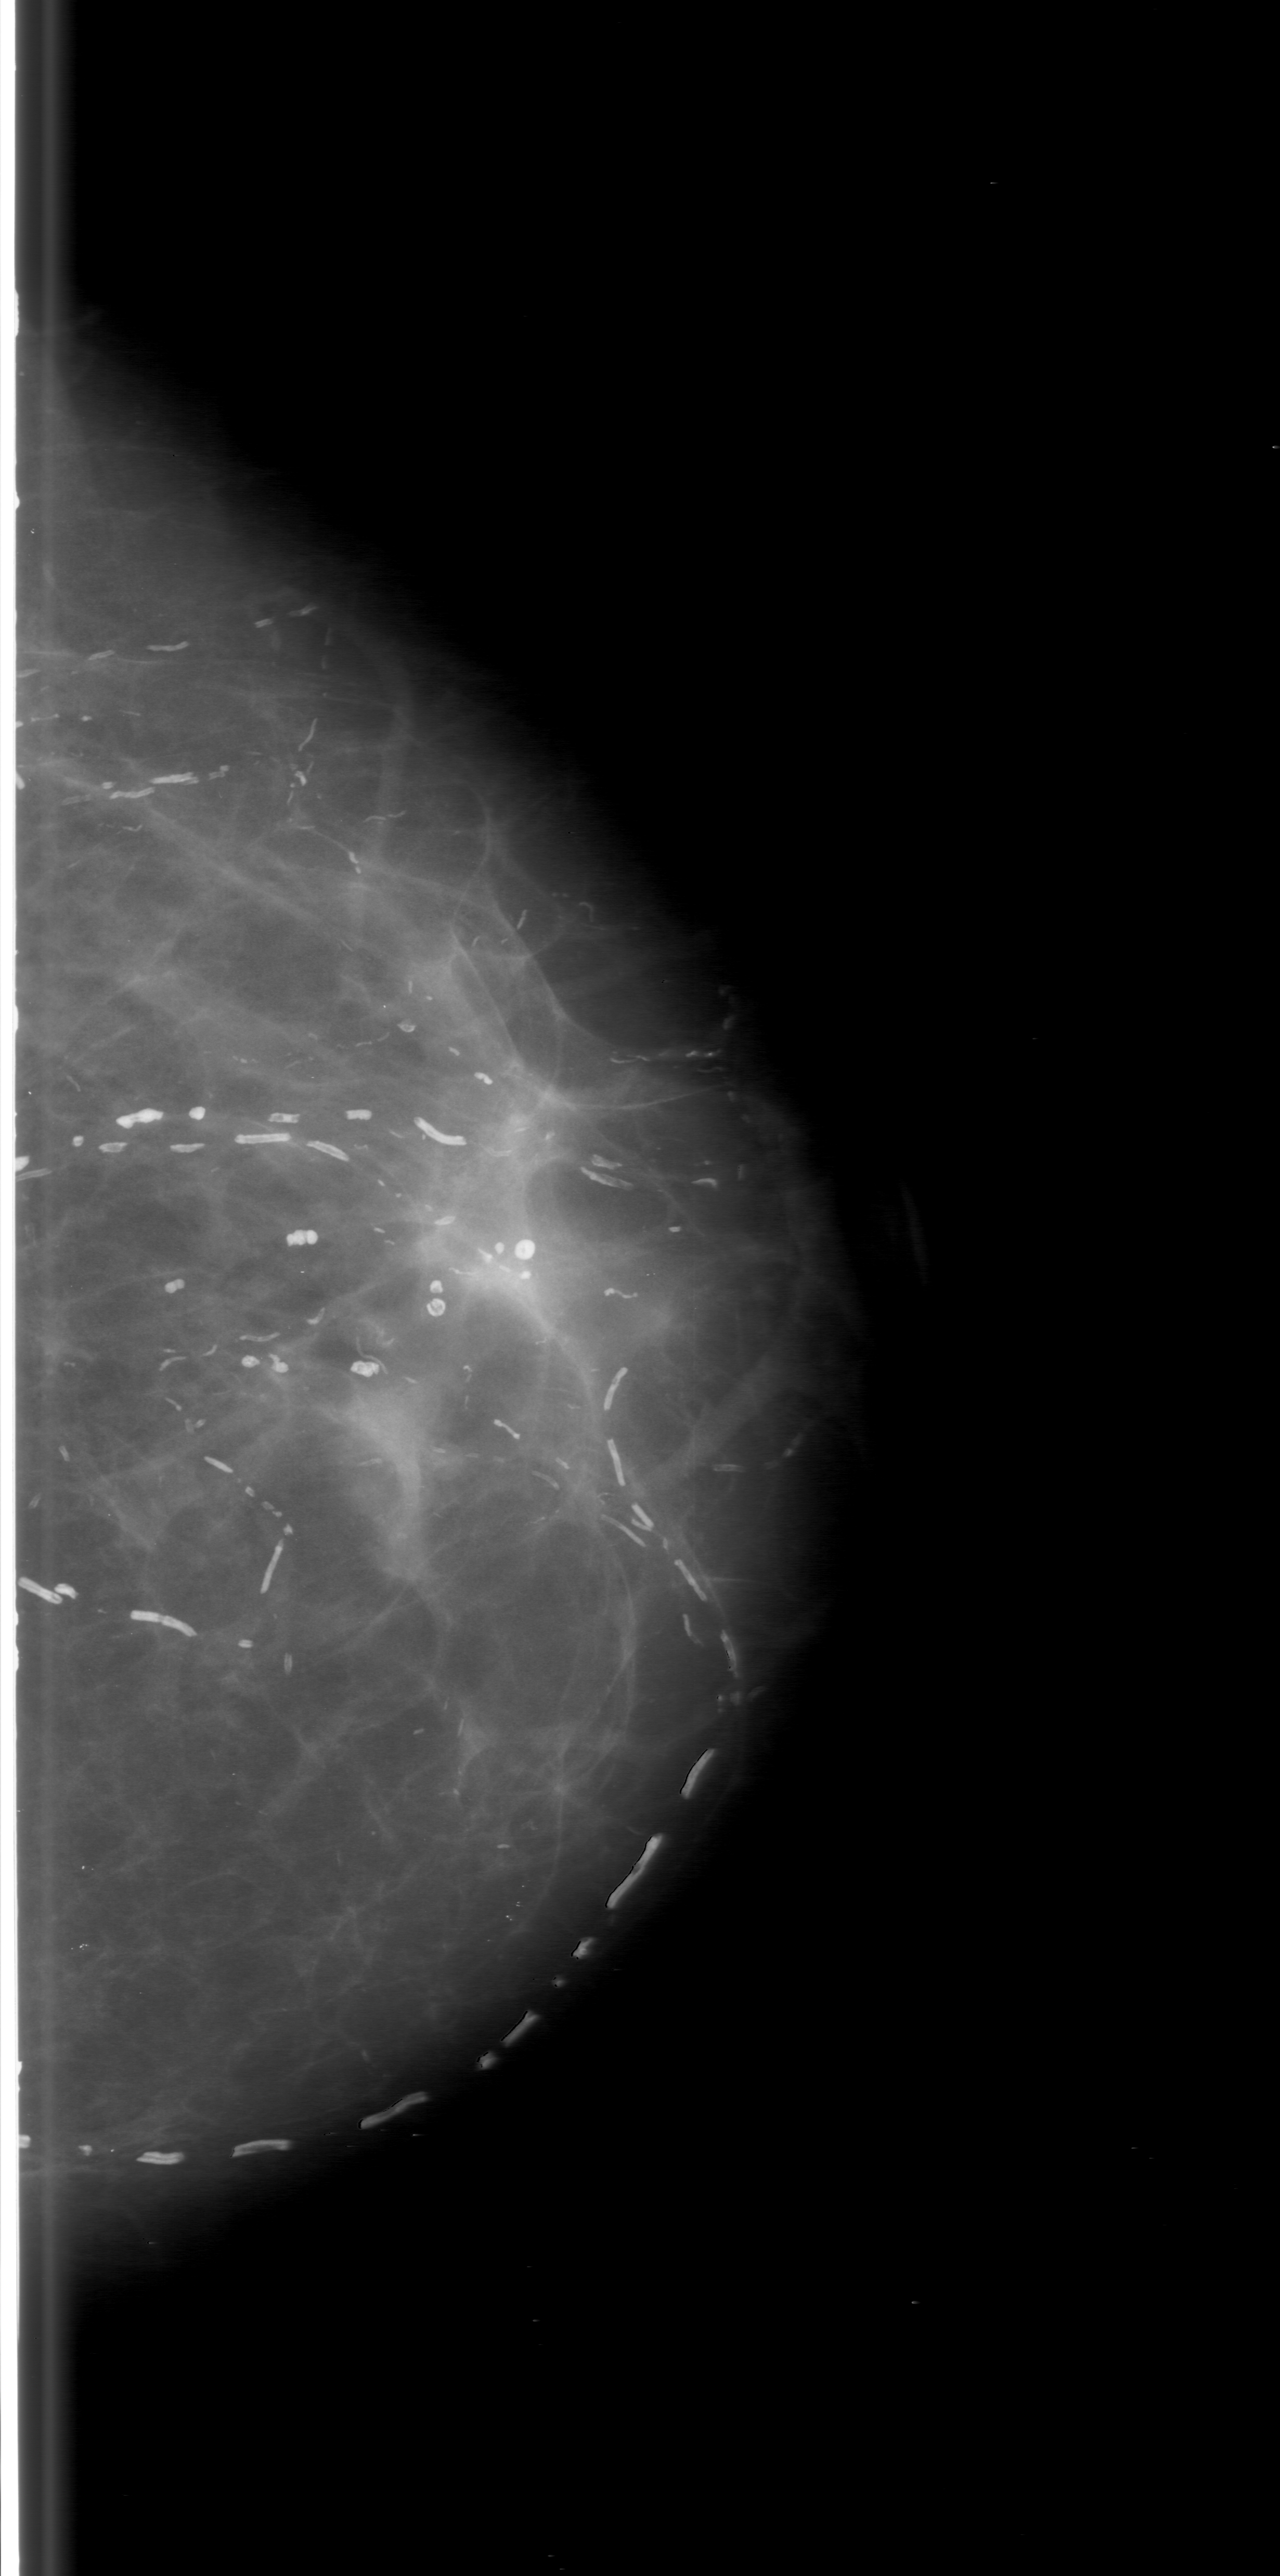
Digitized screen-film mammogram. Left breast. CC view. Breast composition: scattered fibroglandular densities (BI-RADS density category 2 of 4). 1280 × 2576 image matrix.
Marked abnormalities (boxes around the expert regions of interest):
- mass, shape irregular, margins ill defined; BI-RADS assessment category 3; subtlety rating 3 on a 1 (subtle) to 5 (obvious) scale; pathology (as recorded): malignant: bounding box <292,1355,509,1581> (left, top, right, bottom; pixels)